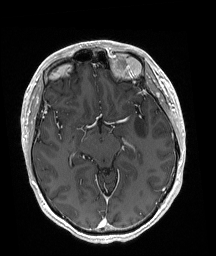
Brain MRI from a brain-tumour surgery series, one axial slice; T1-weighted post-contrast; 1 mm slice thickness; 216 × 256 image matrix, field of view 211 × 250 mm. Case-level facts recorded for this patient, not image findings: histopathology: Astrocytoma; WHO grade: 3; IDH mutation: yes.
Outlined on this slice (manually delineated by an expert):
- tumour: box from (x=134, y=116) to (x=147, y=139) px